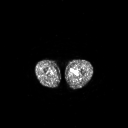
FDG PET of an extremity soft-tissue mass (from a PET/CT study), one axial slice; slice 223 of 267 in the series (ordered by position); 3.27 mm slice thickness; 128 × 128 image matrix, field of view 700 × 700 mm. Patient: male, 63 years. Case-level facts recorded for this patient, not image findings: histological type: pleiomorphic liposarcoma; grade: high; site of the primary tumour: left thigh.
Structures marked on this image (expert contour drawn on MRI and transferred to this co-registered scan by the dataset authors):
- gross tumour volume including surrounding oedema: bounding box <73,69,78,75> (left, top, right, bottom; pixels)